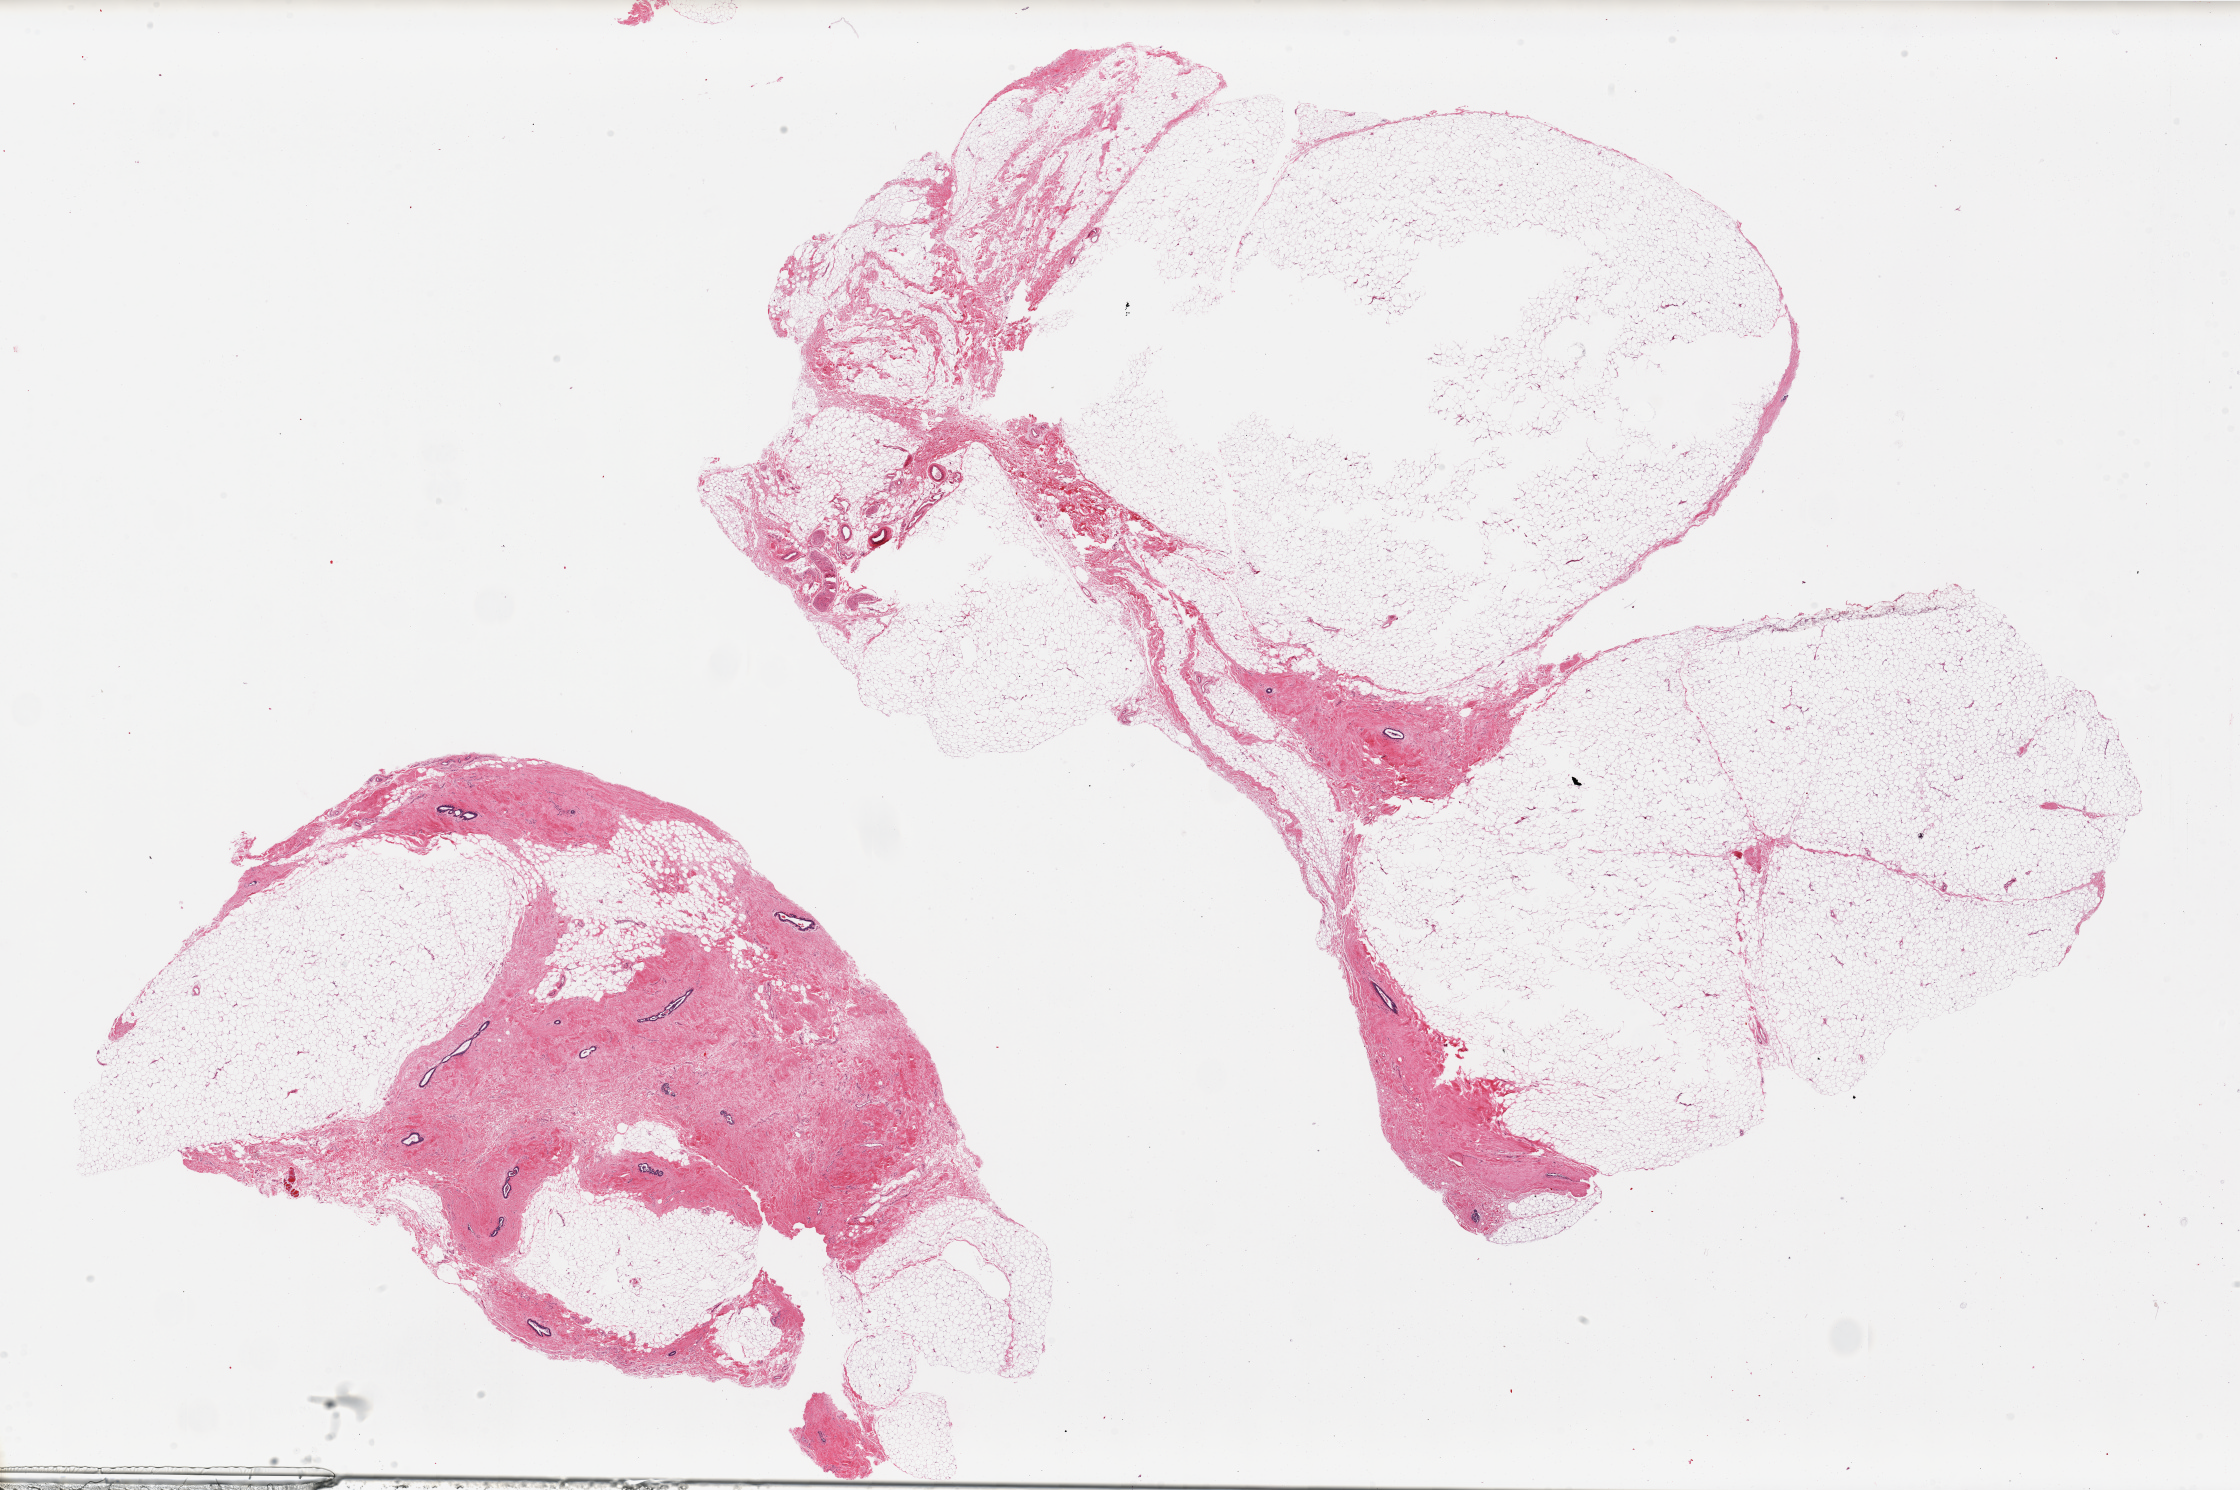
Whole-slide image, haematoxylin and eosin stain — low-resolution overview of the scanned area, about 35.4 x 23.6 mm, PAXgene-fixed paraffin-embedded (PFPE) section, section of breast (target tissue), tissue donor sample. Donor: male.
• pathologist's review note for this sample: 2 pieces; some gynecomastoid hyperplasia (fibrosis and ducts)